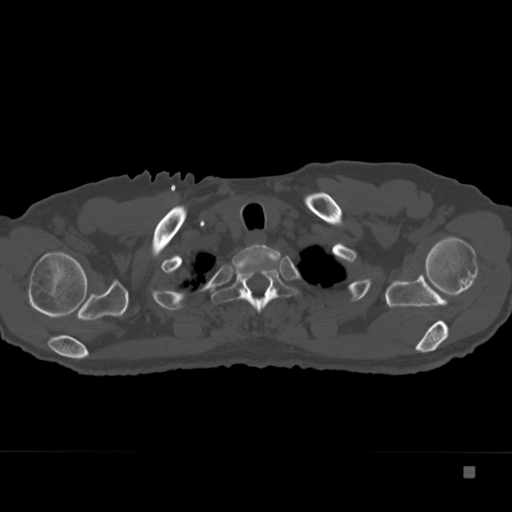
CT including the spine, one axial slice. Reconstruction kernel Br40s. Bone window (W 1800 / L 400 HU). 1.5 mm slice thickness. 512 × 512 image matrix, field of view 389 × 389 mm. Patient: male, 72 years. From the clinical record (not read from this slice): primary cancer: skeletal.
Annotated regions visible in this slice (semi-automatically segmented with operator editing):
- T1 vertebra: box from (x=232, y=244) to (x=281, y=300) px
- T2 vertebra: (x=211, y=262)–(x=298, y=313)